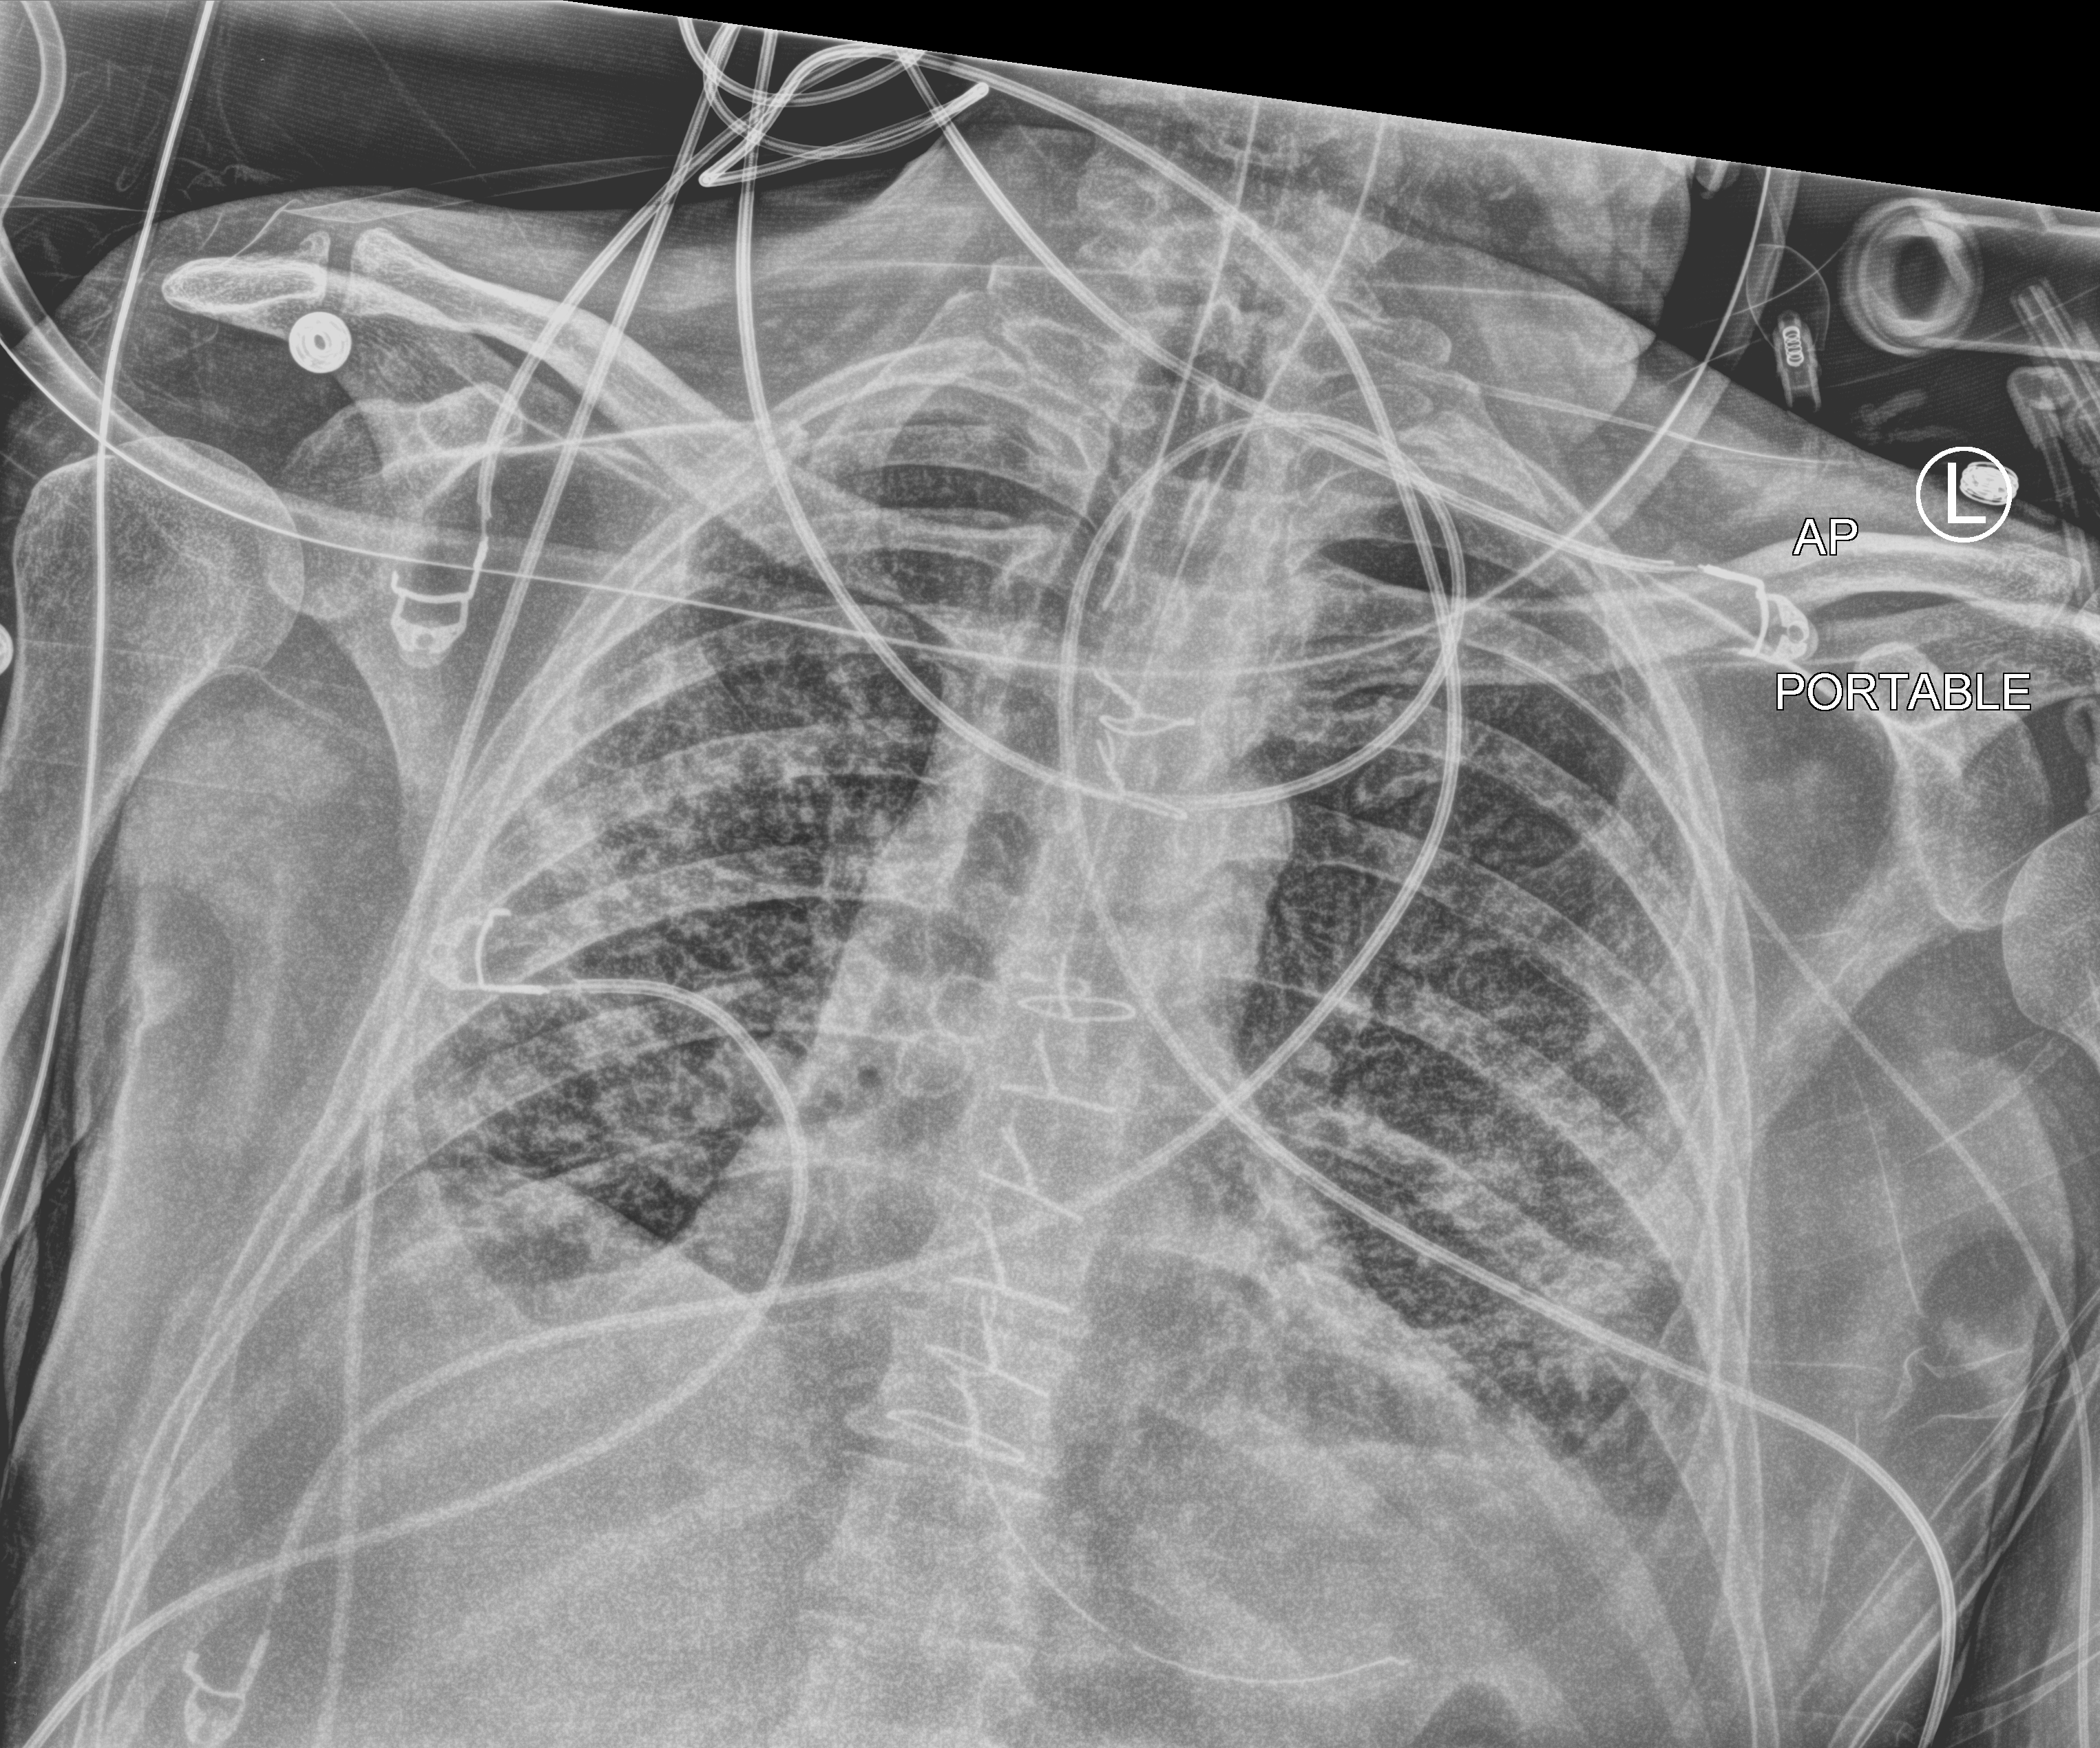
Bedside chest radiograph (computed radiography). Male patient hospitalised with COVID-19, age 18–59 years.
Hospital-stay facts (about this admission, not read from this image; timing relative to this image not recorded): admitted to intensive care during this hospital stay: yes; hypertension (admission record): no; other chronic lung disease (admission record): yes.